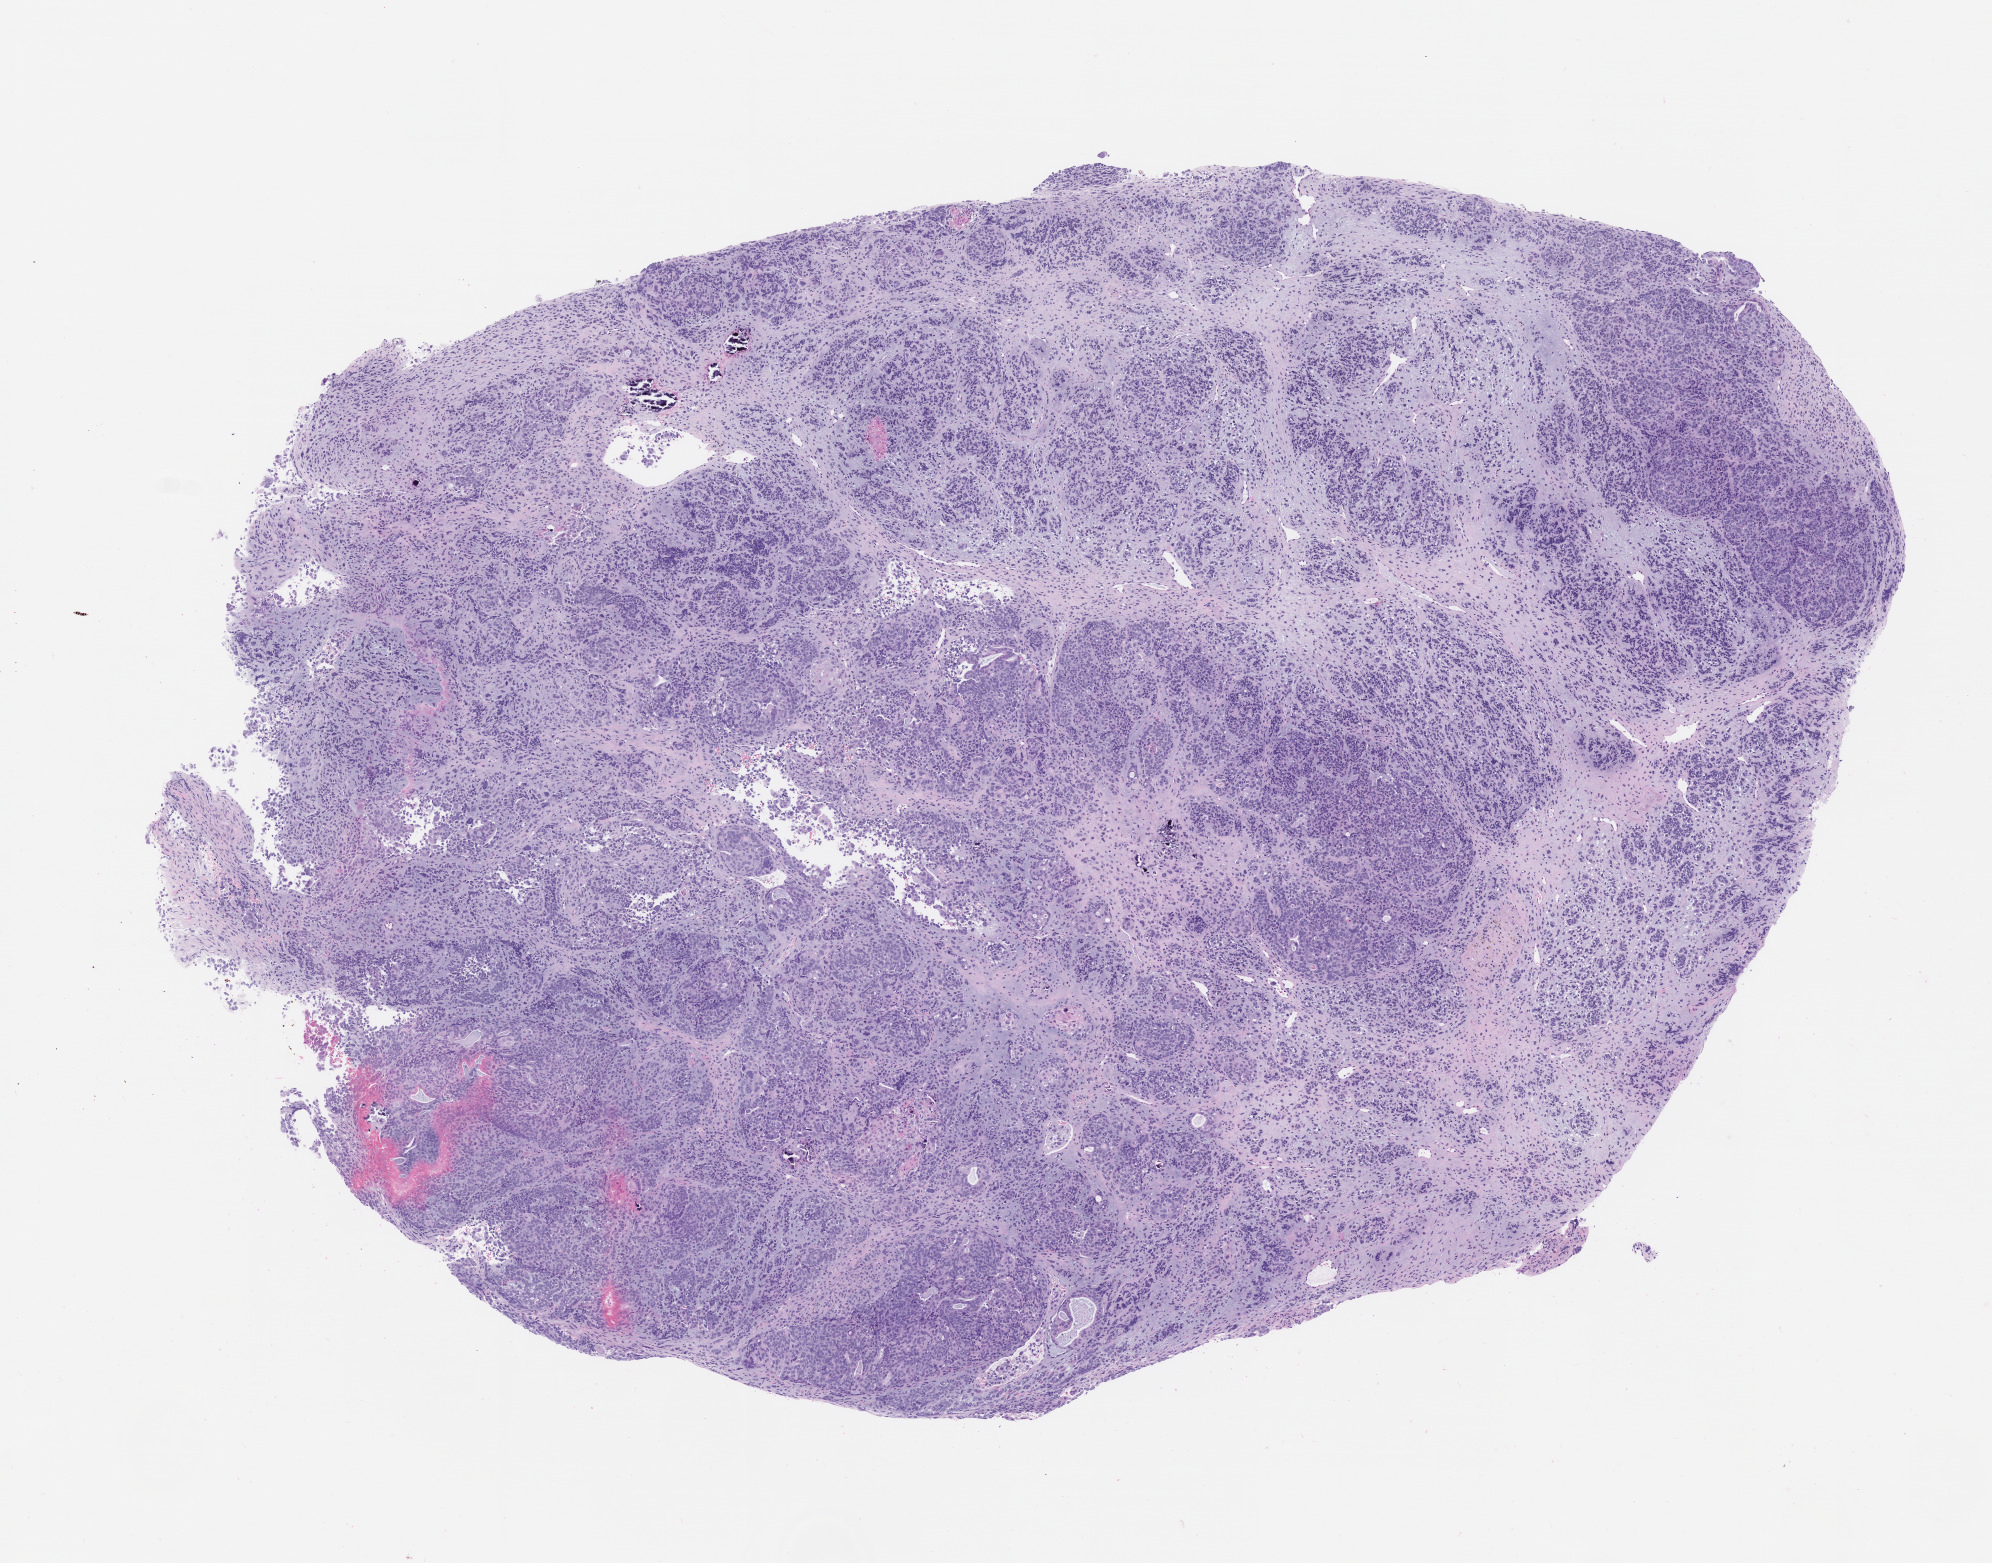
H&E whole-slide image of a patient-derived xenograft (PDX) tumor grown in a mouse, passage 0, low-resolution overview of the scanned area, about 8.0 x 6.3 mm; formalin-fixed paraffin-embedded section; tumor site category: female genital tract.
Originating patient diagnosis: Carcinosarcoma.